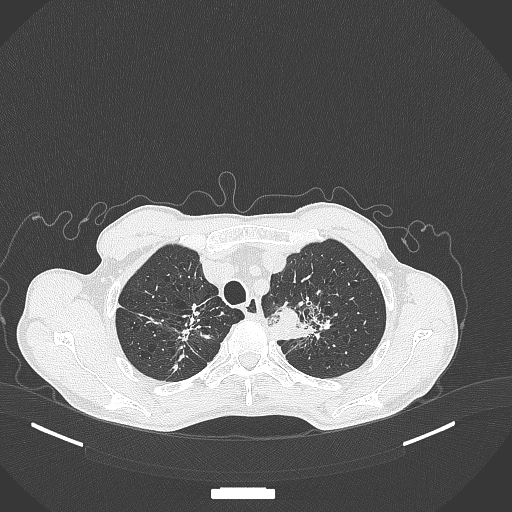
Chest CT, one axial slice. Position 360 of 386 along the scan axis. Reconstruction kernel B70f. 120 kVp. Lung window (W 1500 / L -600 HU). 1 mm slice thickness. 512 × 512 image matrix. Patient: male, 65 years. From the clinical record (not read from this slice): clinical TNM (as recorded): T2b N0 M0; histopathological grade: G2.
Outlined on this slice (rectangle marked by the reading radiologist):
- lung tumour (recorded histology: adenocarcinoma): bounding box (x1, y1, x2, y2) in pixels: (267, 300, 304, 336)